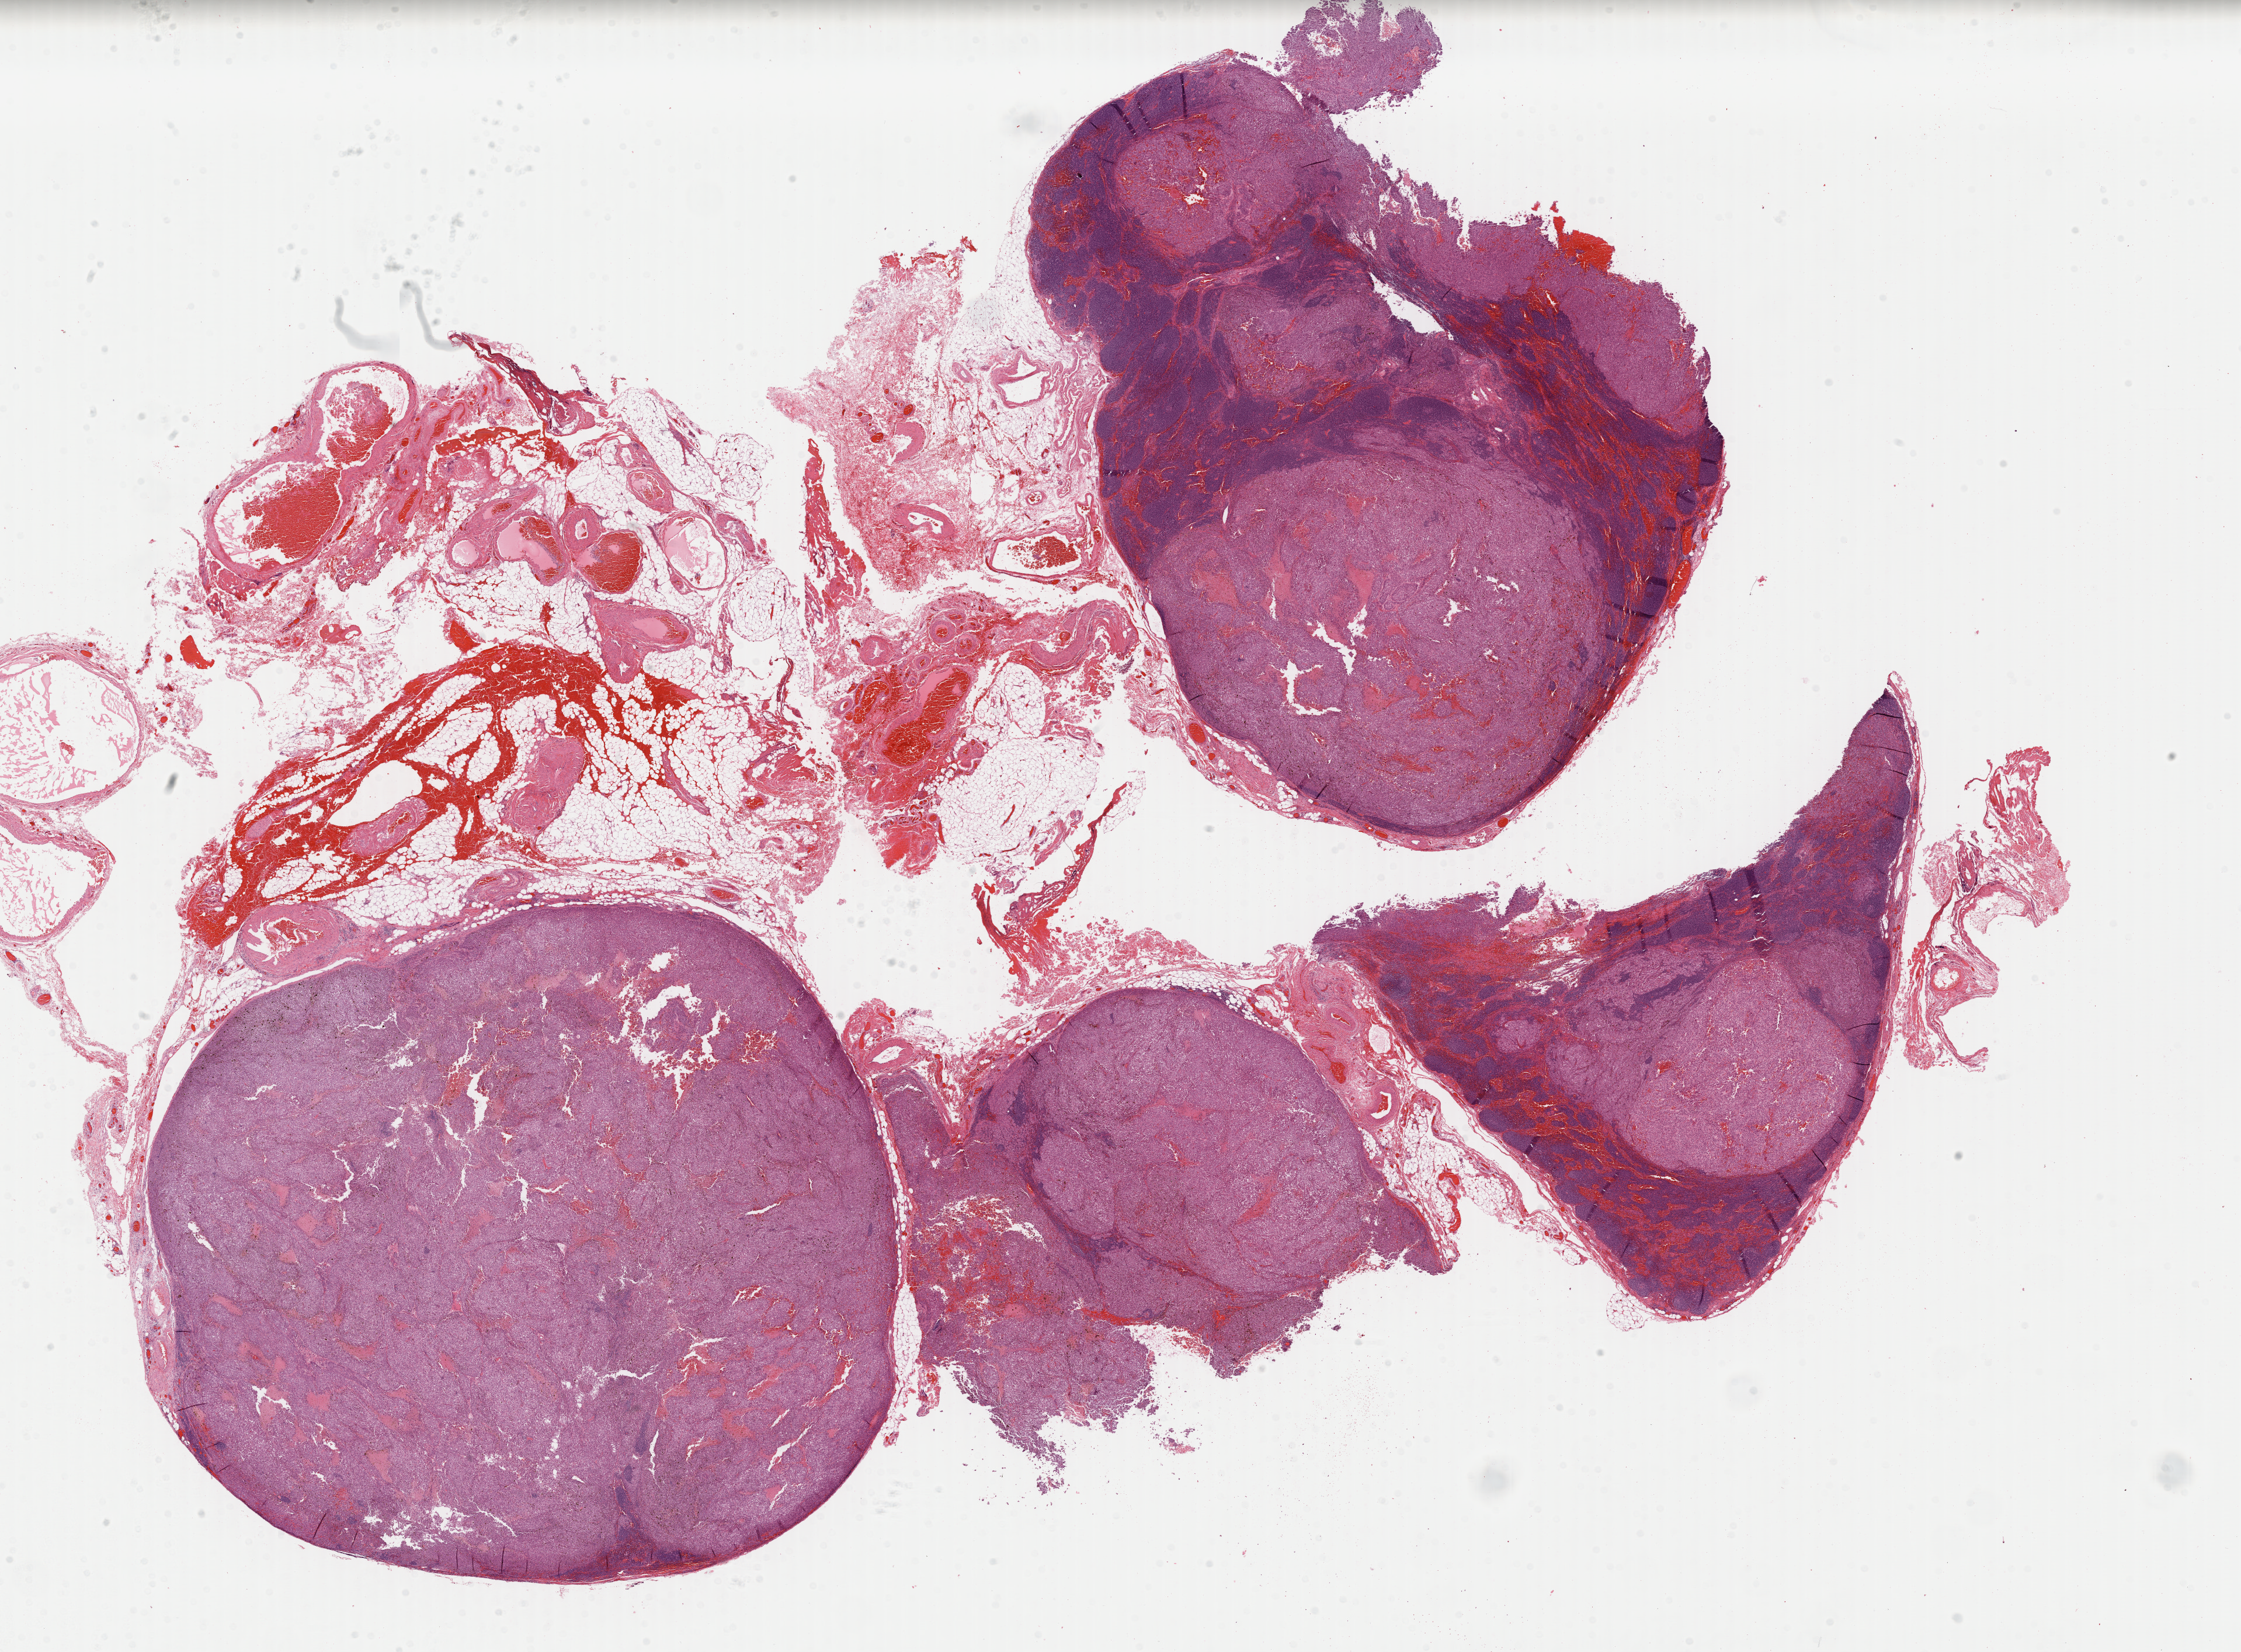
Whole-slide histology image, H&E — whole scanned area (about 30.3 x 22.3 mm) shown as a low-resolution overview; formalin-fixed paraffin-embedded (FFPE) diagnostic section; metastatic tumour sample. Patient: female, age at initial diagnosis 56 years.
- this section: metastatic tumour tissue
- patient diagnosis: Malignant melanoma, NOS